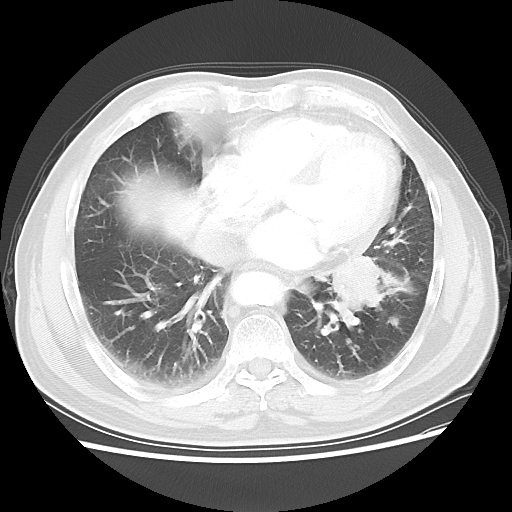
Chest CT, one axial slice; slice 23 of 56 in the series (ordered by position); reconstruction kernel LUNG; 120 kVp; lung window (W 1500 / L -600 HU); 5 mm slice thickness; 512 × 512 image matrix, field of view 360 × 360 mm. Patient: male, 75 years. From the clinical record (not read from this slice): clinical TNM (as recorded): T3 N0 M0.
Structures marked on this image (bounding box drawn by a radiologist):
- lung tumour (recorded histology: squamous cell carcinoma): bounding box [x1, y1, x2, y2] px = [315, 242, 395, 324]